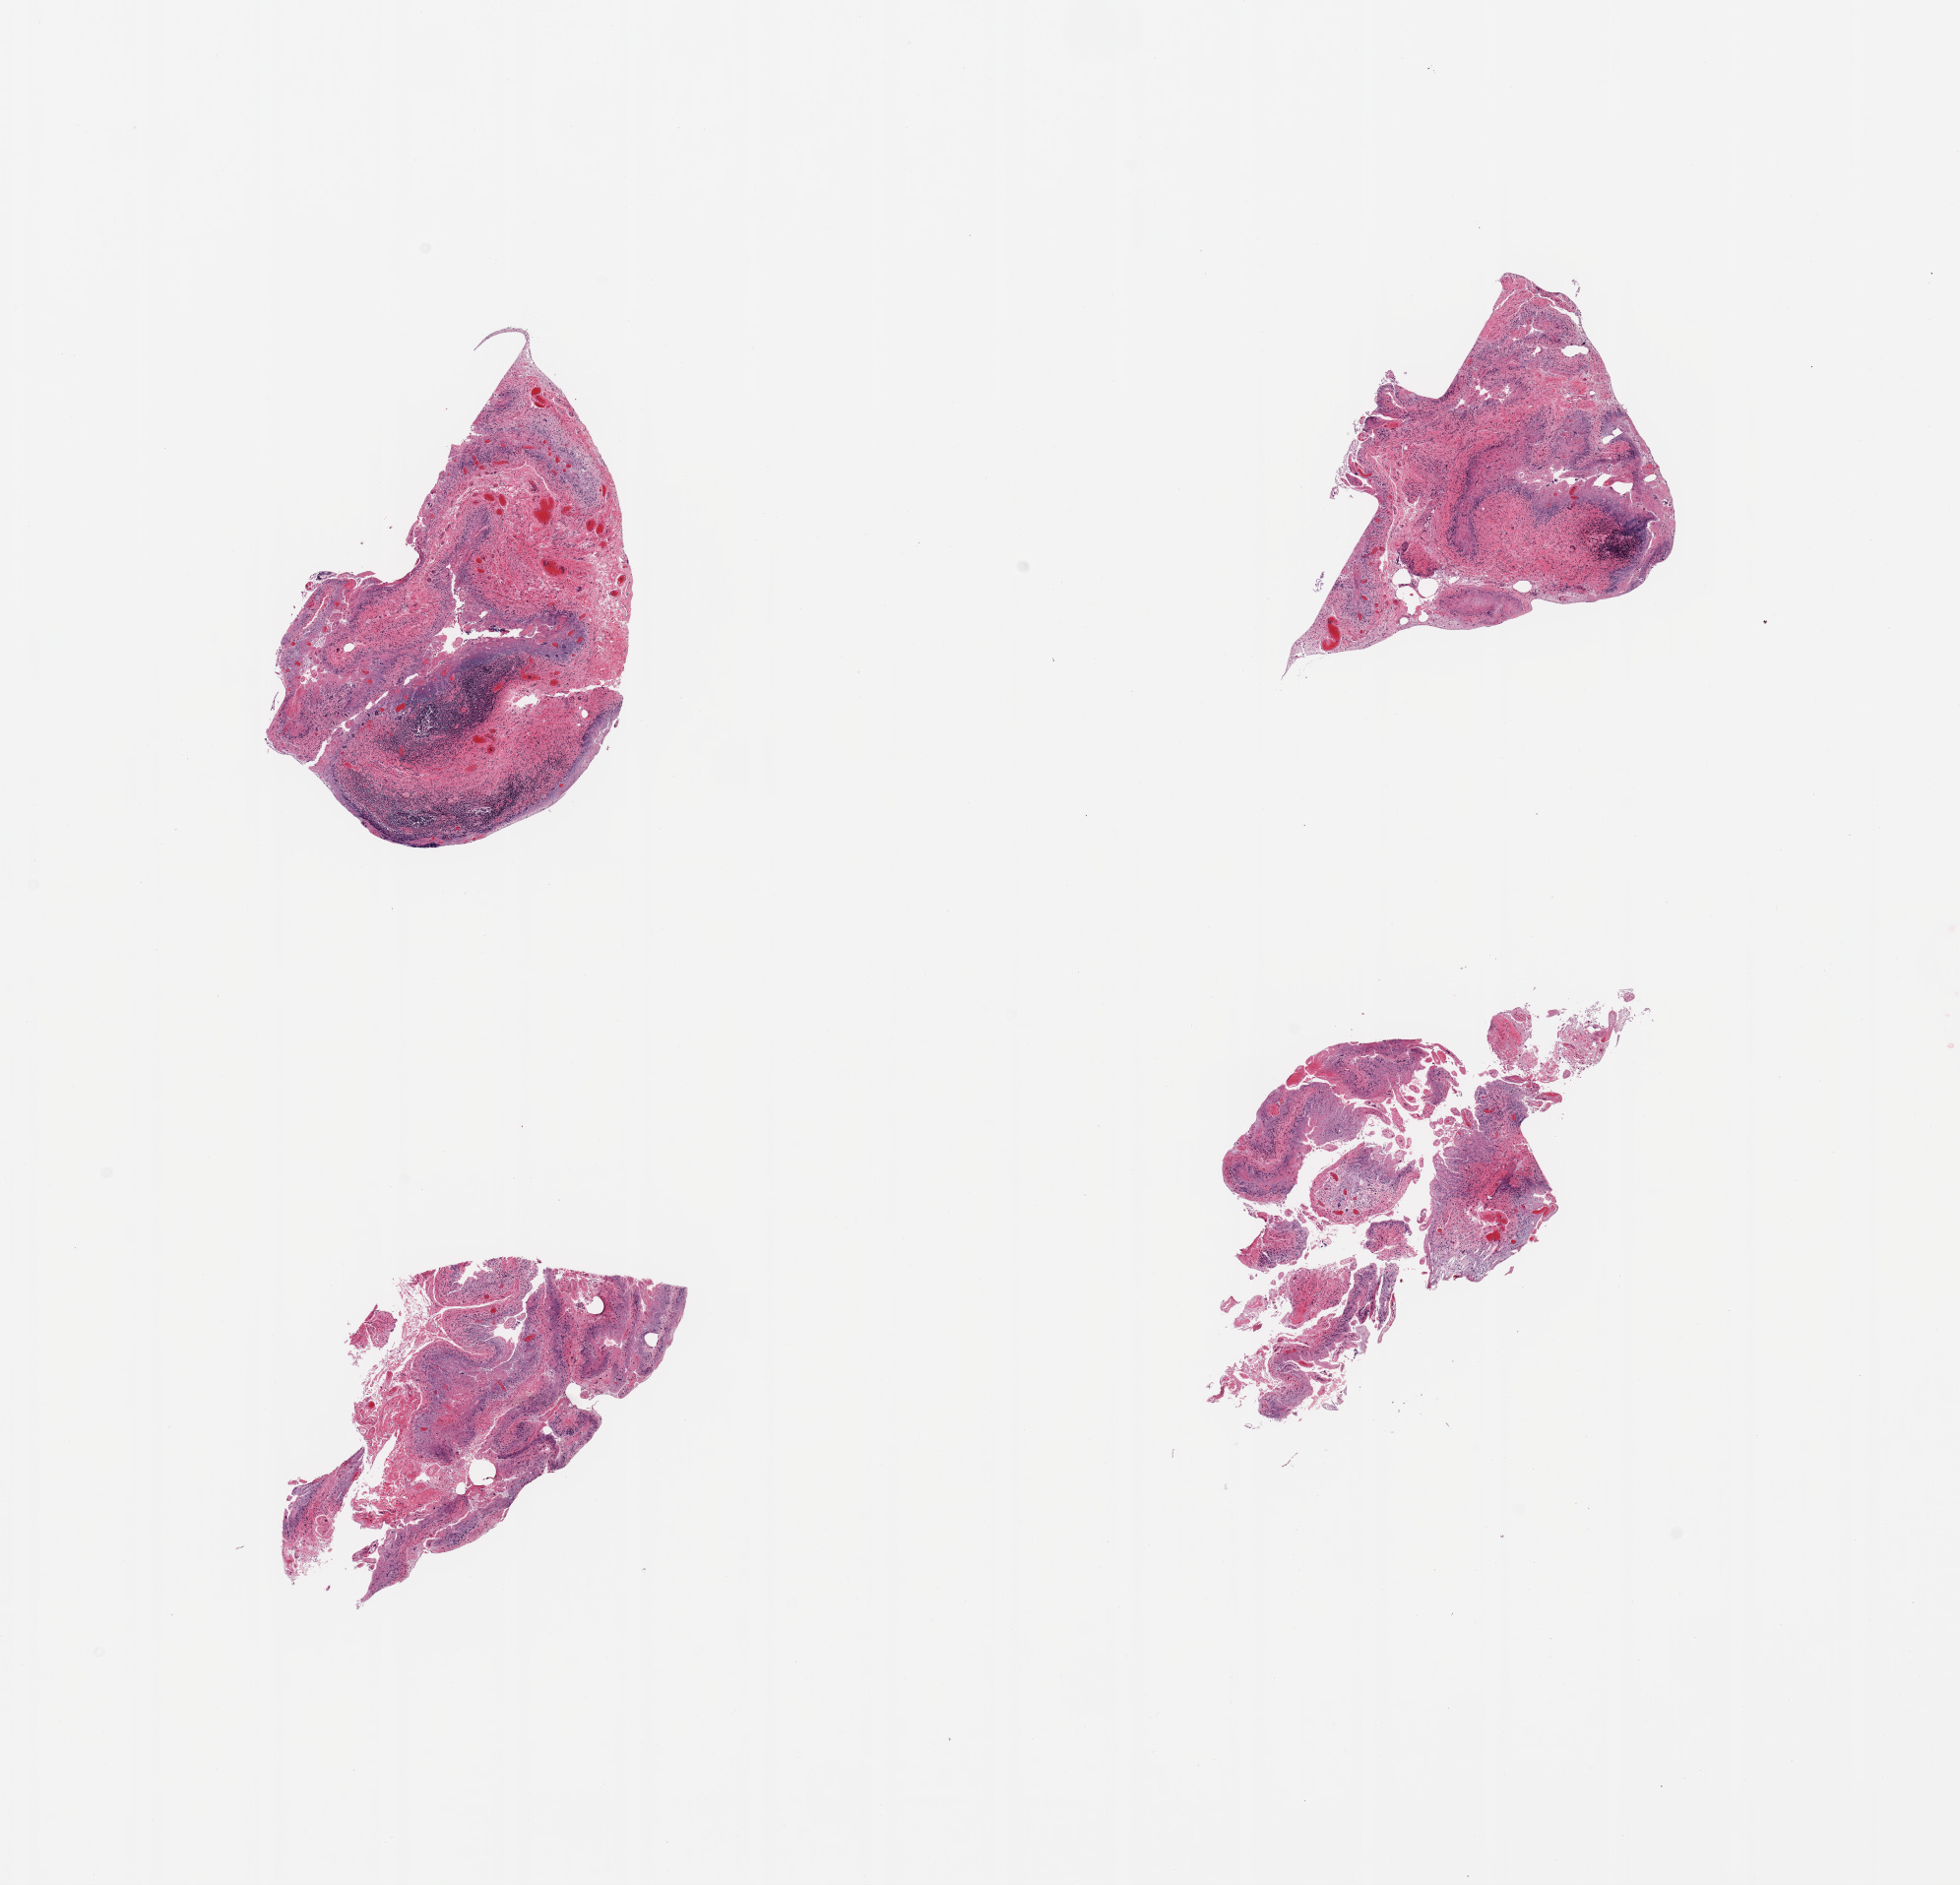
Whole-slide image, haematoxylin and eosin stain, brightfield — a low-resolution overview of the entire scanned area, about 15.8 x 15.1 mm; PAXgene-fixed, paraffin-embedded tissue; sampled site (target tissue): ileum; donor tissue sample.
- reviewer comment on this tissue sample: 4 pieces; predominantly autolyzed mucosa with few residual foci of lymphoid tissue, submucosa